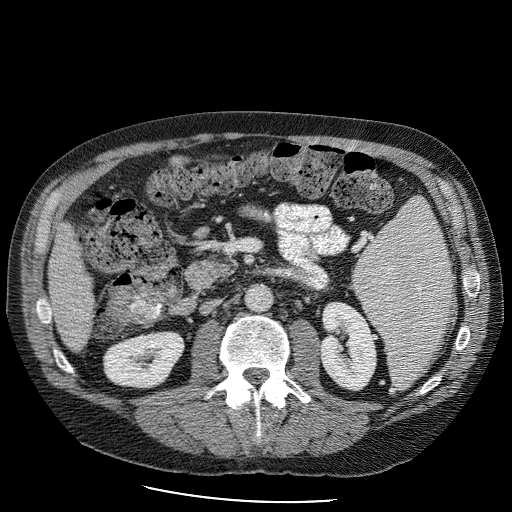
Contrast-enhanced abdominal CT (liver protocol), one axial slice. Position 29 of 98 along the scan axis. Reconstruction kernel STANDARD. Soft-tissue window (W 400 / L 40 HU). 2.5 mm slice thickness. 512 × 512 image matrix. Case-level facts recorded for this patient, not image findings: diagnosis: hepatocellular carcinoma (patient treated with transarterial chemoembolisation; whether this scan precedes or follows treatment is not stated here); TNM stage (as recorded): Stage-II; Child-Pugh class: B; tumour differentiation: moderately differentiated; tumour nodularity: uninodular.
Annotated regions visible in this slice (semi-automatic segmentation, software-assisted and operator-edited):
- liver parenchyma outside the tumour (the mass and vessels are separate outlines, so this box may not span the whole liver): bounding box <46,215,100,348> (left, top, right, bottom; pixels)
- liver vessels: <76,311,80,313>